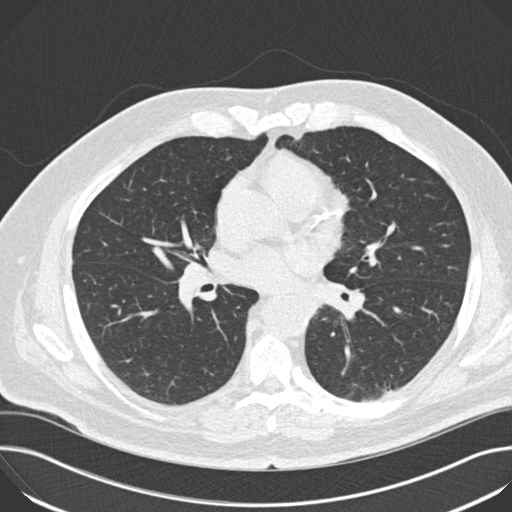
Chest CT (low-dose screening protocol), one axial image, third screening round (two years after baseline), lung window (W 1500 / L -600 HU), 2 mm slice thickness, 512 × 512 image matrix, field of view 380 × 380 mm. Male, age 68 years at enrolment. Current smoker at enrolment.
Lesion marked by an expert reader, bounding box <149,237,237,314> (left, top, right, bottom; pixels). No non-calcified nodule or mass ≥4 mm was recorded by the screening reader at this exam. Official screen result: negative screen, no significant abnormalities. Participant outcome: lung cancer diagnosed 151 days after this screen — small cell carcinoma, NOS, right hilum, mediastinum, stage IV (AJCC 6th edition).